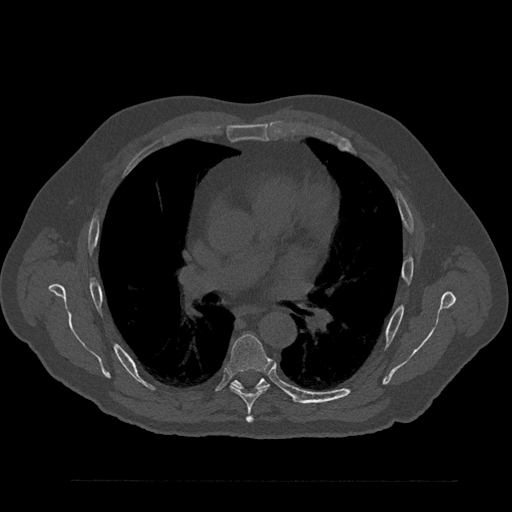
CT including the spine, one axial slice. Slice 539 of 797 in the series (ordered by position). Reconstruction kernel Br40s/3. 120 kVp. Bone window (W 1800 / L 400 HU). 512 × 512 image matrix, field of view 430 × 430 mm. Patient: male, 61 years. Case-level facts recorded for this patient, not image findings: primary cancer: prostate.
Structures marked on this image (semi-automatic segmentation, software-assisted and operator-edited):
- T6 vertebra: box from (x=228, y=334) to (x=272, y=423) px
- T7 vertebra: (x=233, y=378)–(x=269, y=389)